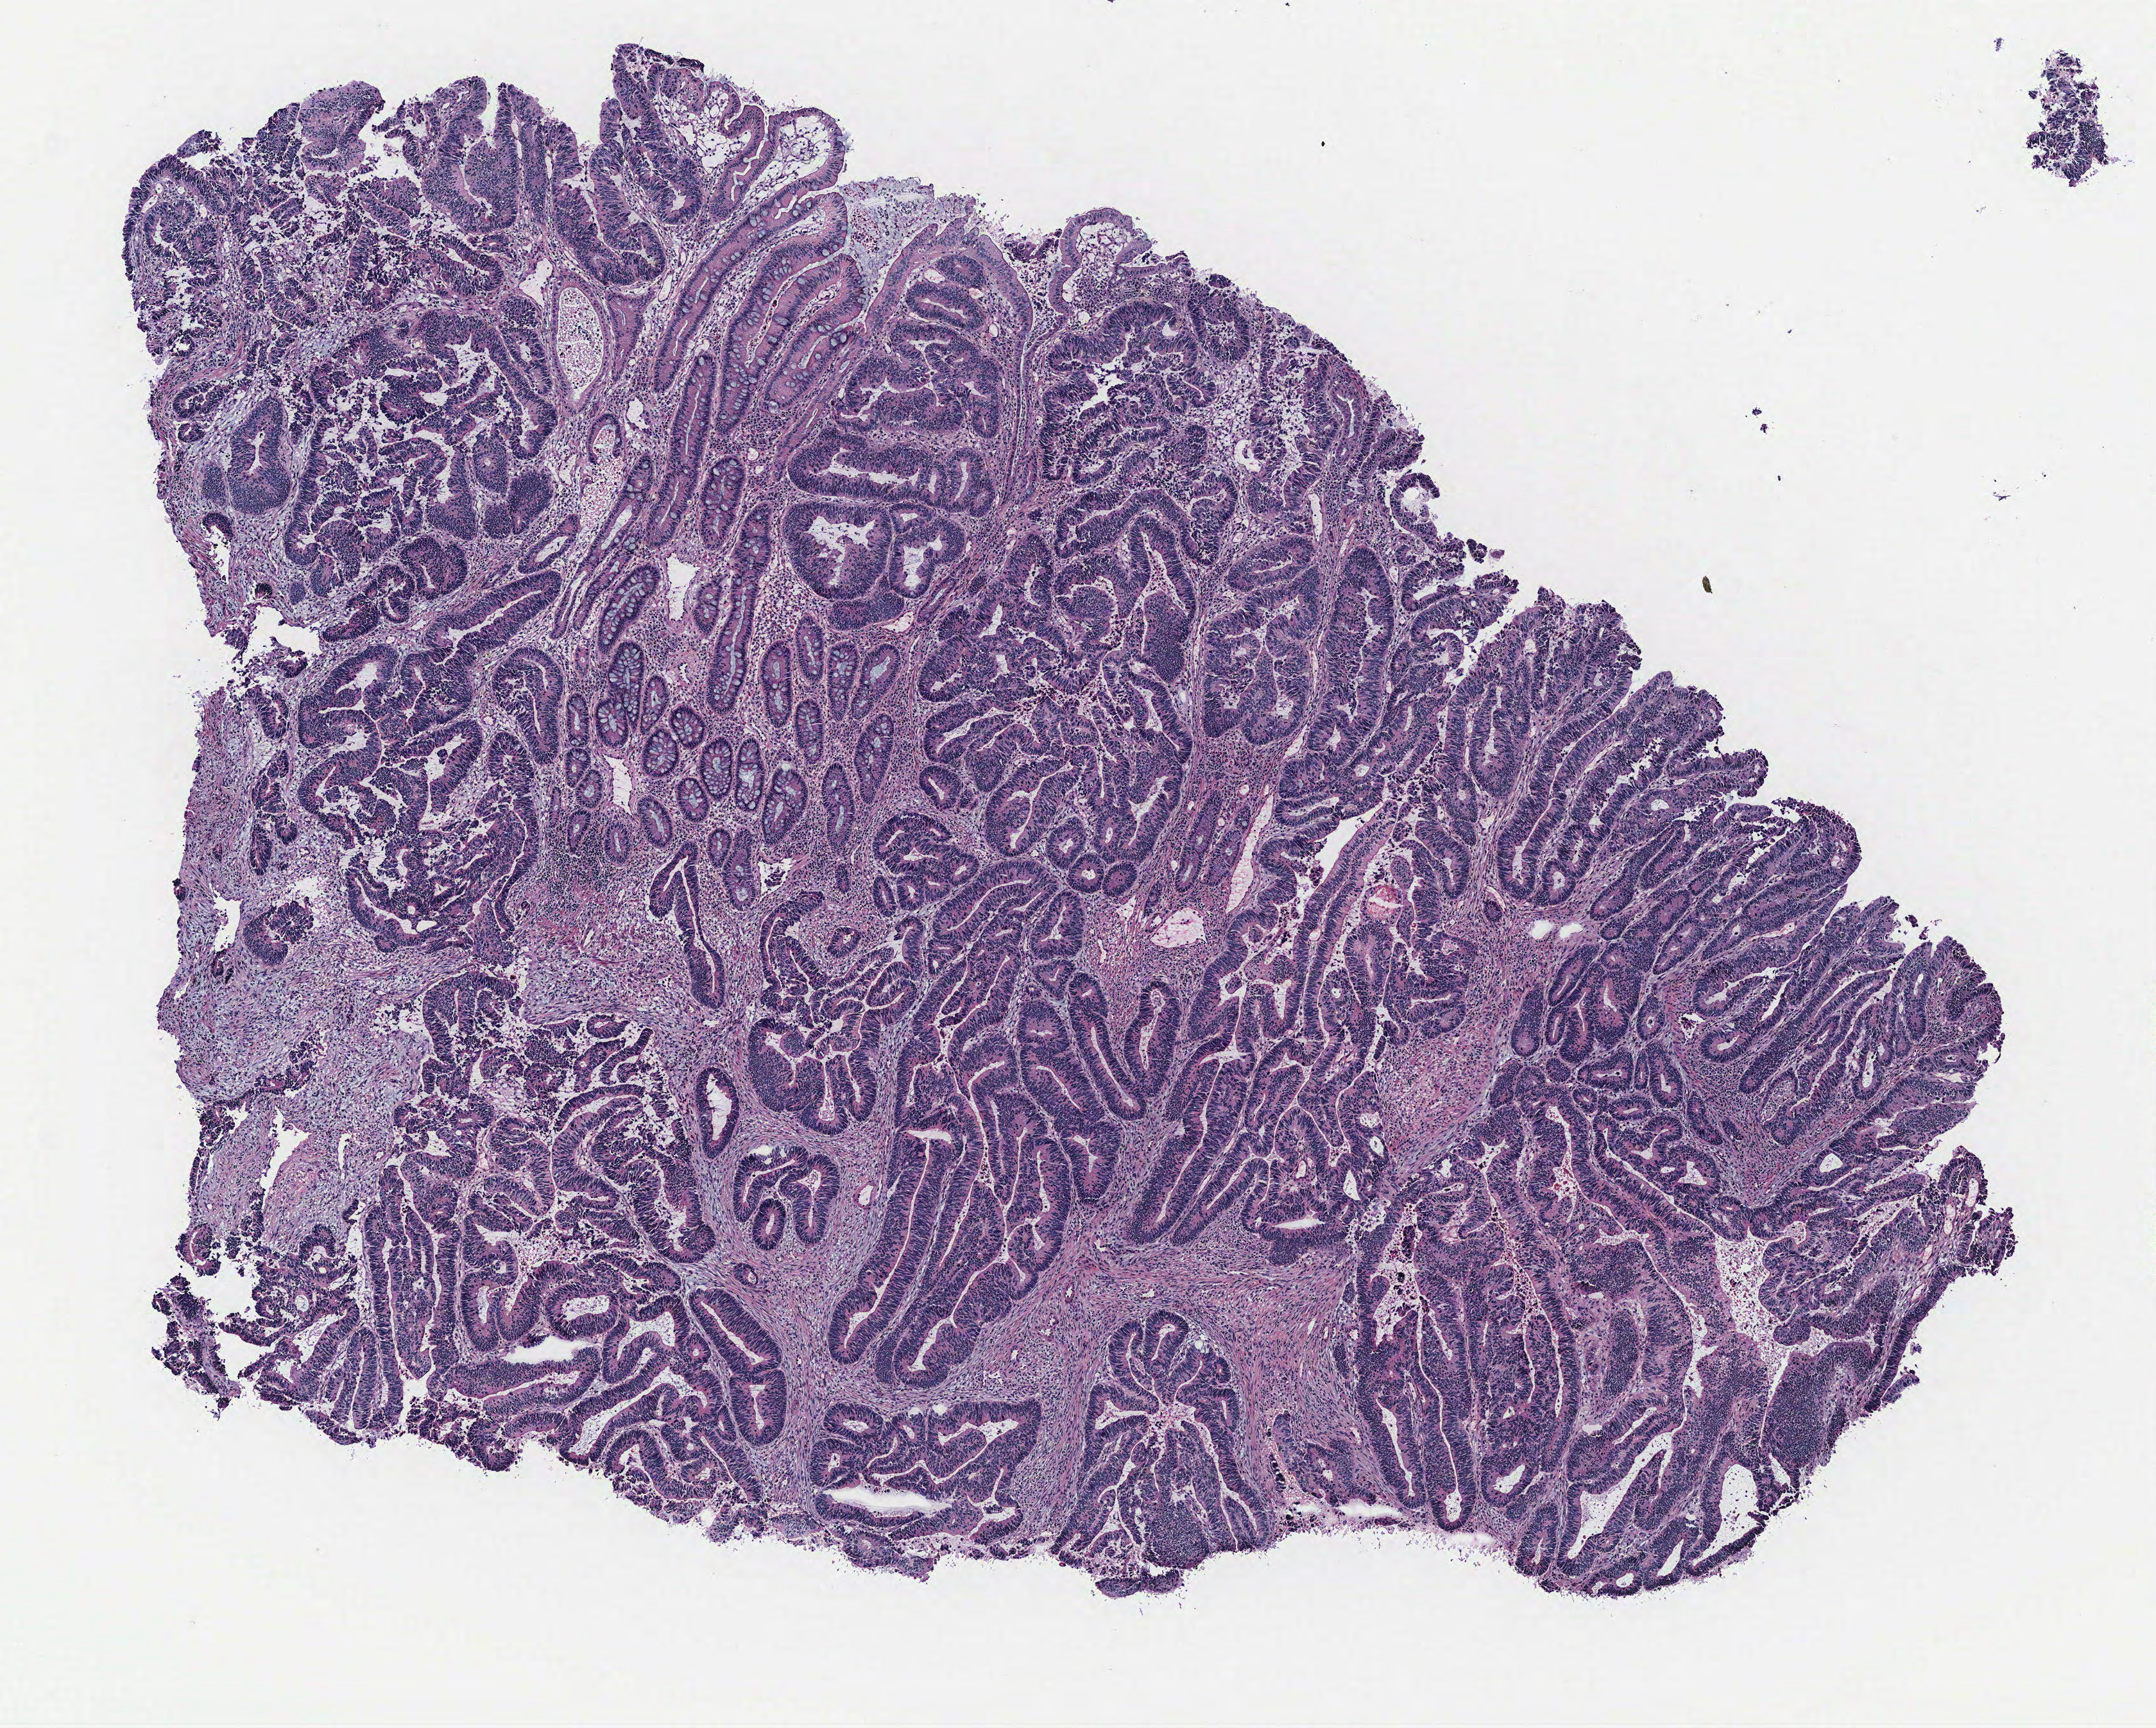
Hematoxylin and eosin (H&E) stained whole-slide image — a low-resolution overview of the entire scanned area, about 6.7 x 5.4 mm (acquisition: 40x scan). Colon, tissue type not recorded.
- patient diagnosis (cohort enrolment): colon cancer (colon)